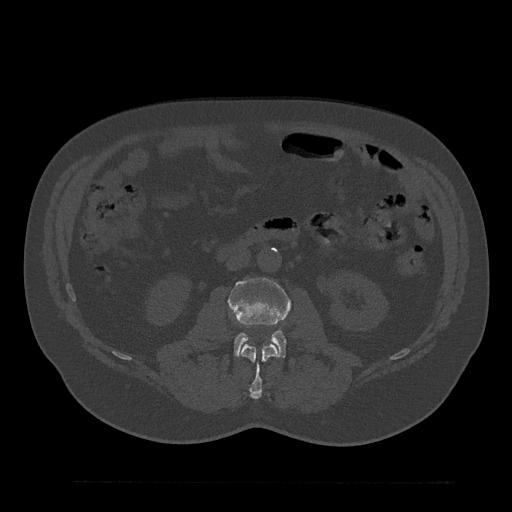
CT including the spine, one axial slice. Position 64 of 797 along the scan axis. Reconstruction kernel Br40s/3. 120 kVp. Bone window (W 1800 / L 400 HU). 0.5 mm slice thickness. 512 × 512 image matrix, field of view 430 × 430 mm. Male patient, age 61 years. From the clinical record (not read from this slice): primary cancer: prostate.
Structures marked on this image (semi-automatic segmentation, software-assisted and operator-edited):
- L2 vertebra: box from (x=241, y=344) to (x=278, y=399) px
- L3 vertebra: (x=229, y=277)–(x=292, y=357)